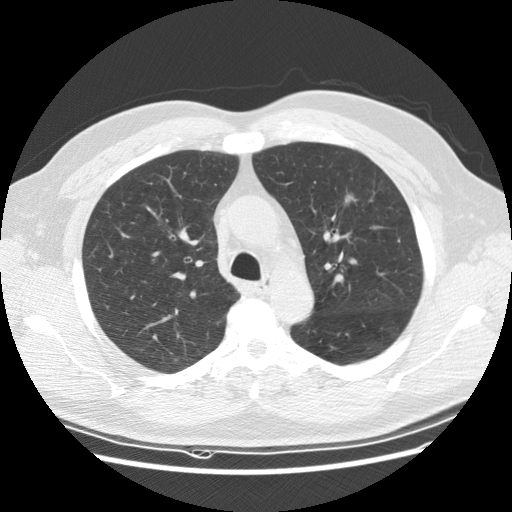
Low-dose screening chest CT, axial slice; baseline annual screen; lung window (W 1500 / L -600 HU); 2.5 mm slice thickness; slice 42 of 152 in the series. Male, age 65 years at enrolment.
- Expert reader's lesion annotation, box from (x=325, y=182) to (x=378, y=225) px.
- The screening reader recorded 2 non-calcified nodules or masses ≥4 mm on this exam (left upper lobe, right upper lobe); which of them this box marks is not recorded.
- Participant outcome: lung cancer diagnosed 488 days after this screen — carcinoma, NOS, left upper lobe, poorly differentiated (G3), stage IIIA (AJCC 6th edition), 25 mm at pathology.